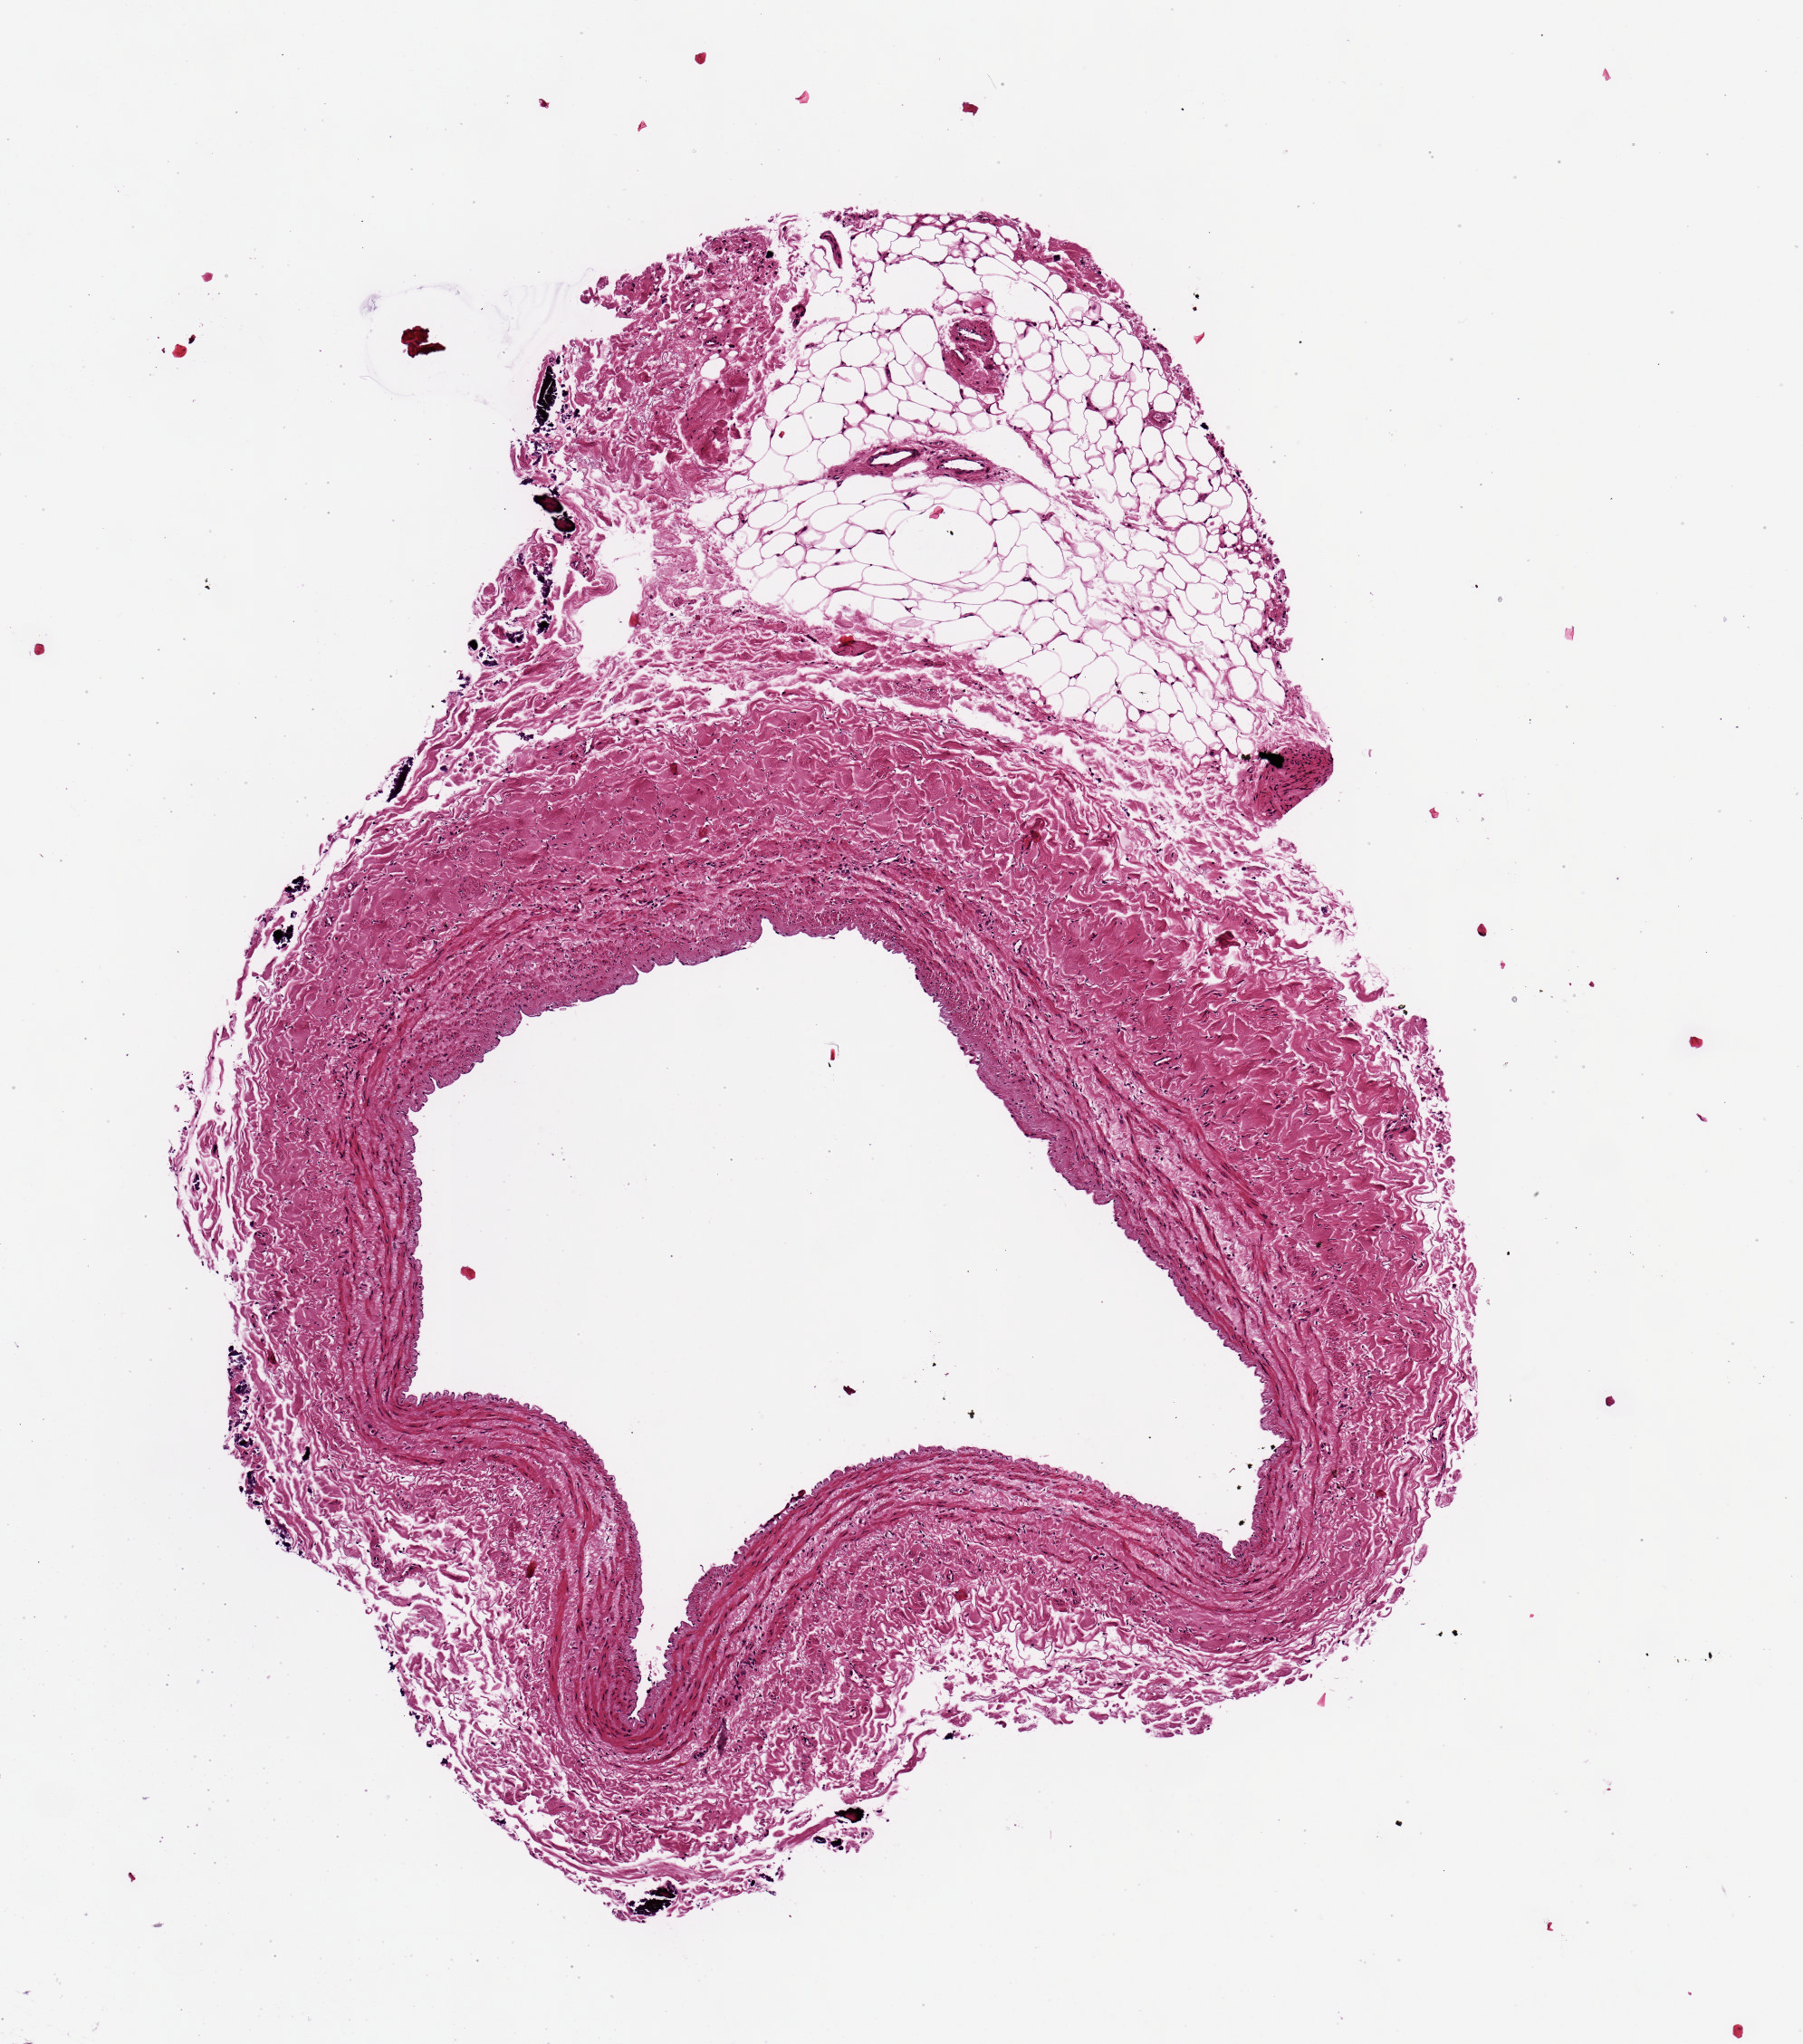
Hematoxylin and eosin (H&E) whole-slide image, brightfield — a low-resolution overview of the entire scanned area, about 3.9 x 4.5 mm (slide scanned at 20x), PAXgene-fixed, paraffin-embedded tissue, section of tibial artery (target tissue), tissue donor sample. Female donor.
Review note (as recorded): 1 x 2mm nodule of fat attached to 2.6 x 2.8mm vessel.